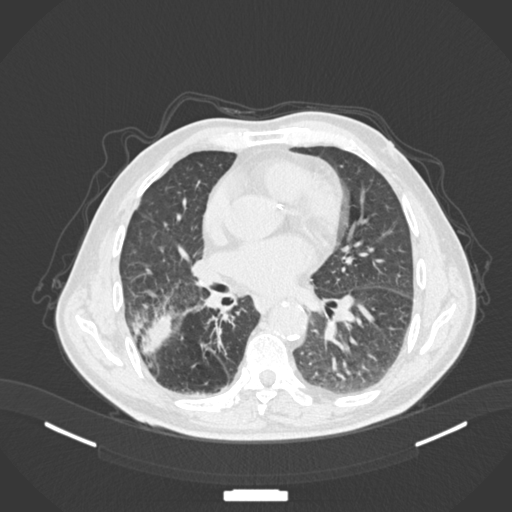
Chest CT, one axial slice. Position 73 of 201 along the scan axis. Reconstruction kernel B30f. 120 kVp. Lung window (W 1500 / L -600 HU). 512 × 512 image matrix. Male patient, age 72 years. From the clinical record (not read from this slice): clinical TNM (as recorded): T3 N2 M0.
Outlined on this slice (bounding box drawn by a radiologist):
- lung tumour (recorded histology: adenocarcinoma): bounding box (x1, y1, x2, y2) in pixels: (136, 313, 174, 359)